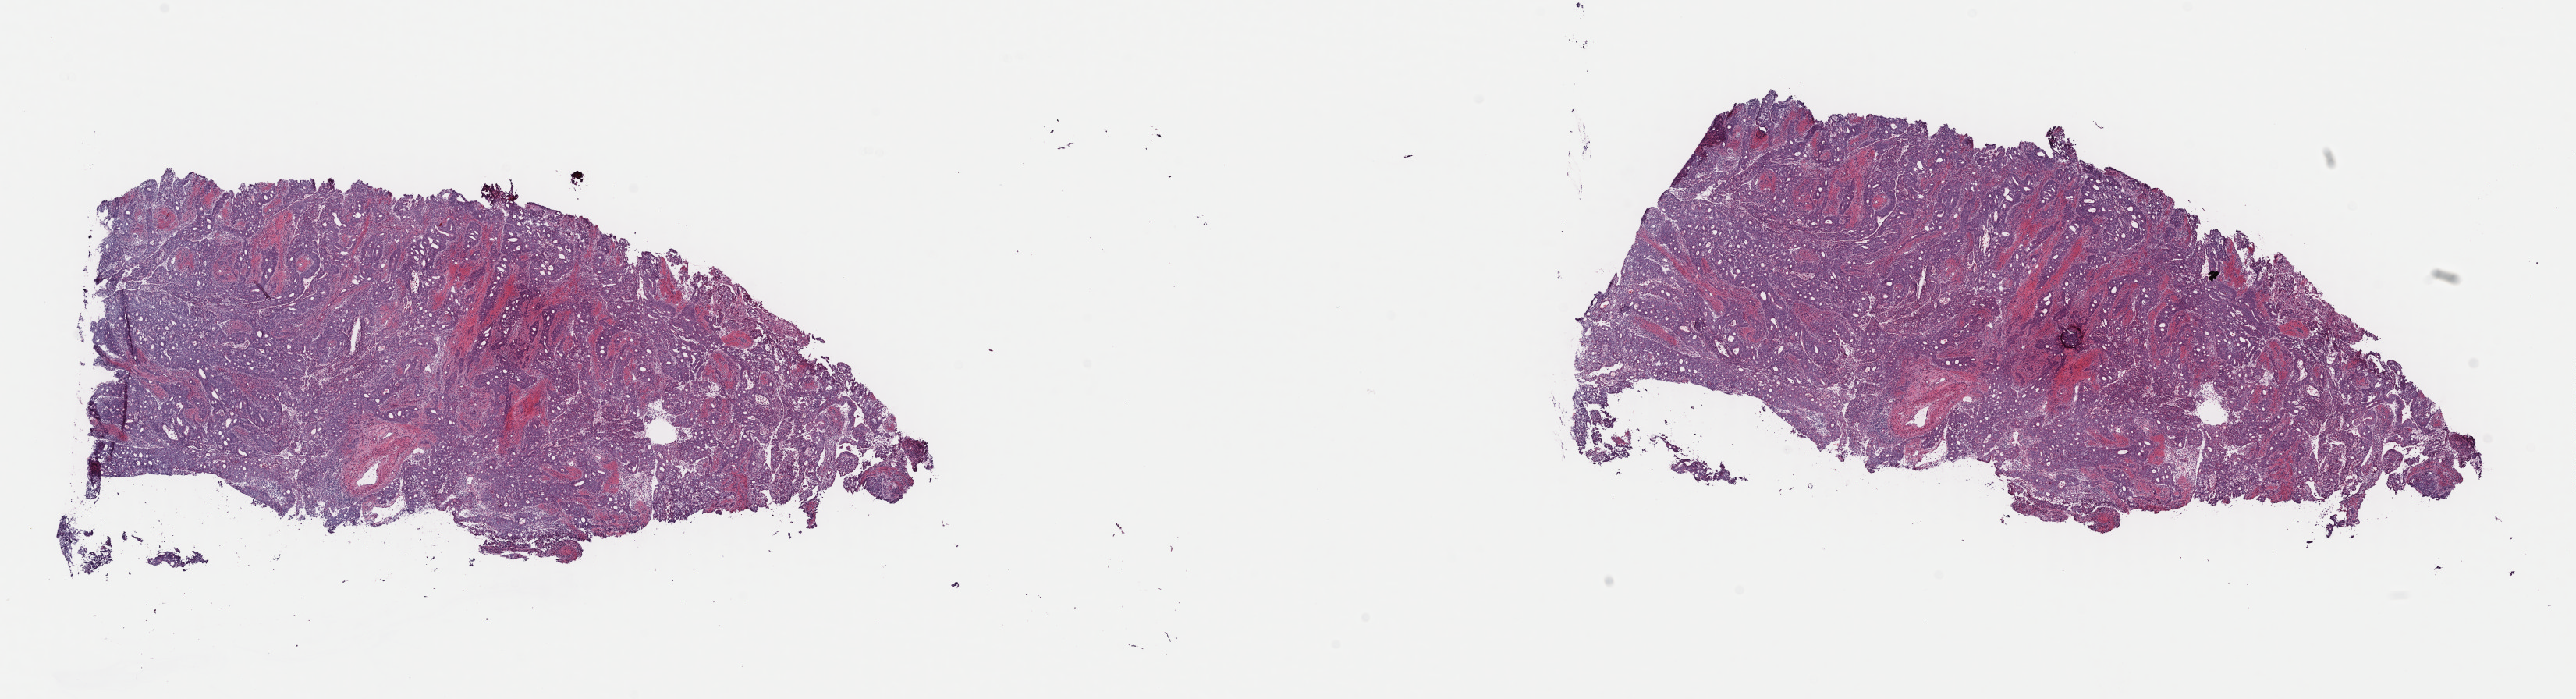
Digitized H&E-stained tissue section (whole slide), shown as a low-resolution overview of the whole scanned area (about 26.0 x 7.1 mm); frozen section from the top of the tissue portion; sample: primary tumour, colon. Patient: male, age at initial diagnosis 58 years. Slide review estimates, as recorded: tumour cells 80%, tumour nuclei 80%, normal cells 0%, stromal cells 20%, necrosis 0%. Inflammatory infiltration, as recorded: lymphocyte infiltration 2%, monocyte infiltration 1%, neutrophil infiltration 4%.
AJCC pathologic stage: IIIC (7th edition). Diagnosis: Adenocarcinoma, NOS (ascending colon).